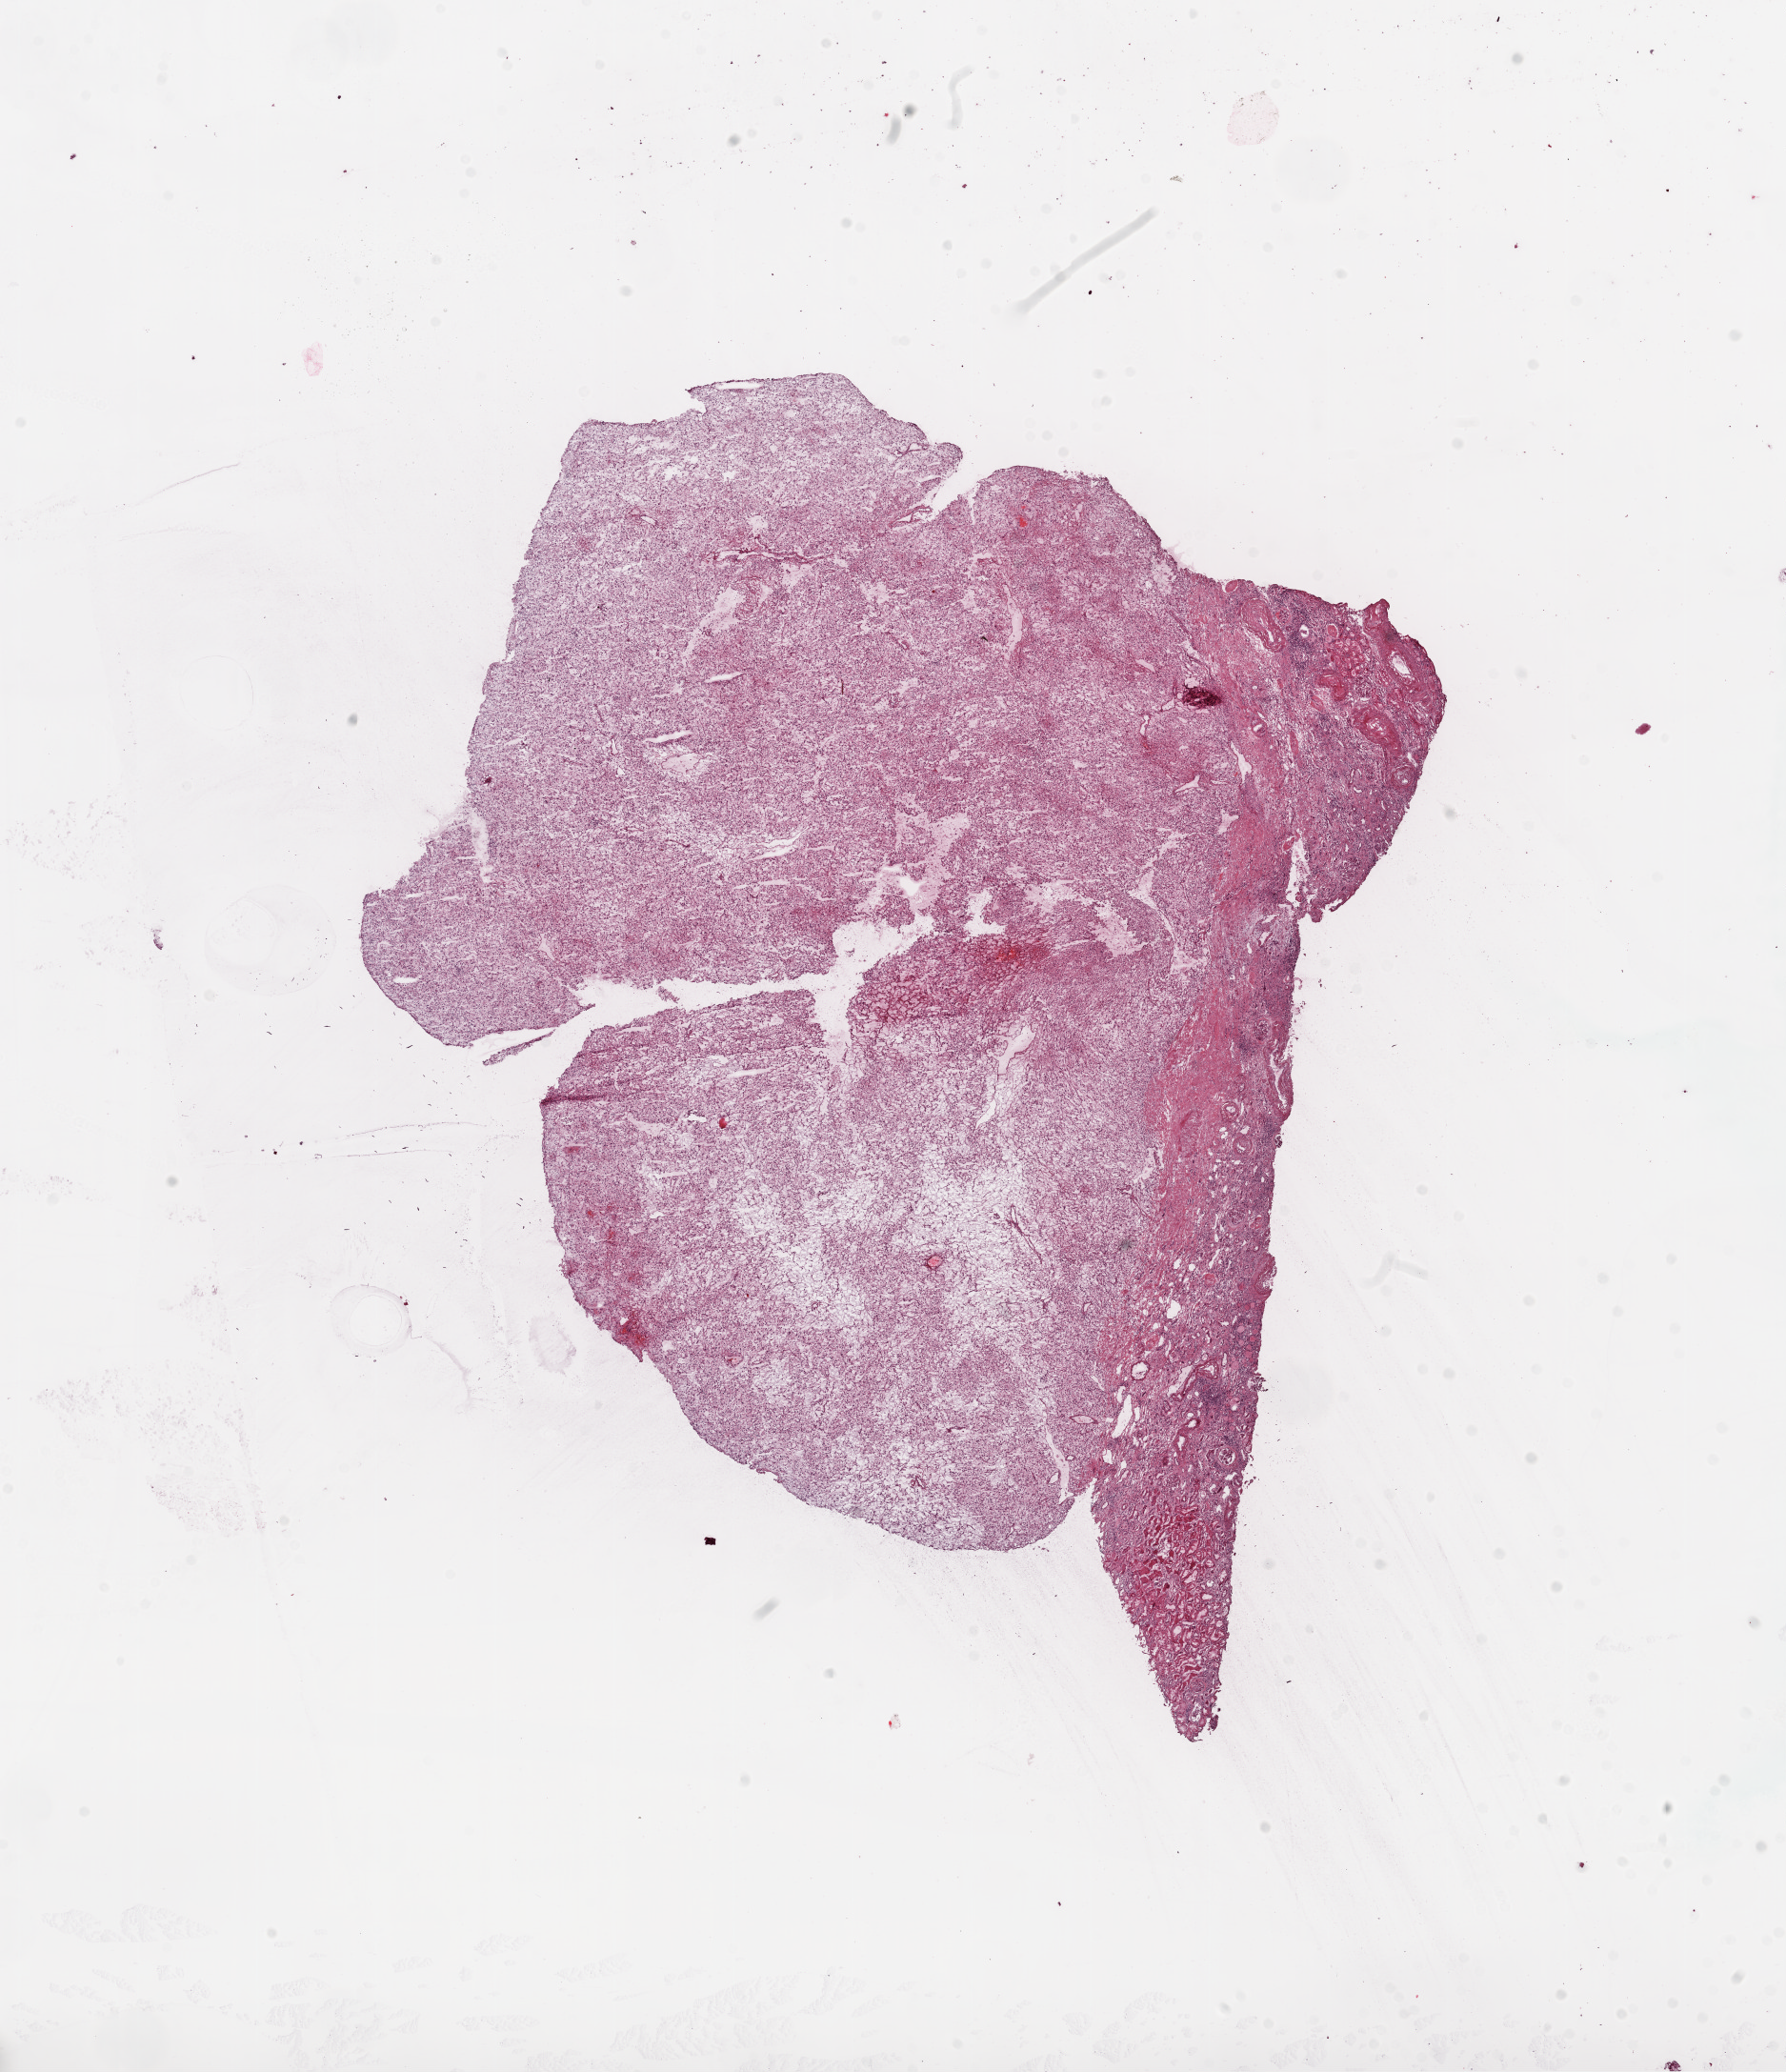
Hematoxylin and eosin (H&E) stained whole-slide image, a low-resolution overview of the entire scanned area, about 15.0 x 17.5 mm (slide scanned at 20x). Frozen section from the top of the tissue portion. Kidney, primary tumour sample. Female, age 79 years at initial diagnosis. Pathologist review of this section (percent, as recorded): tumour cells 76%, tumour nuclei 80%.
Histologic diagnosis: Clear cell adenocarcinoma, NOS.